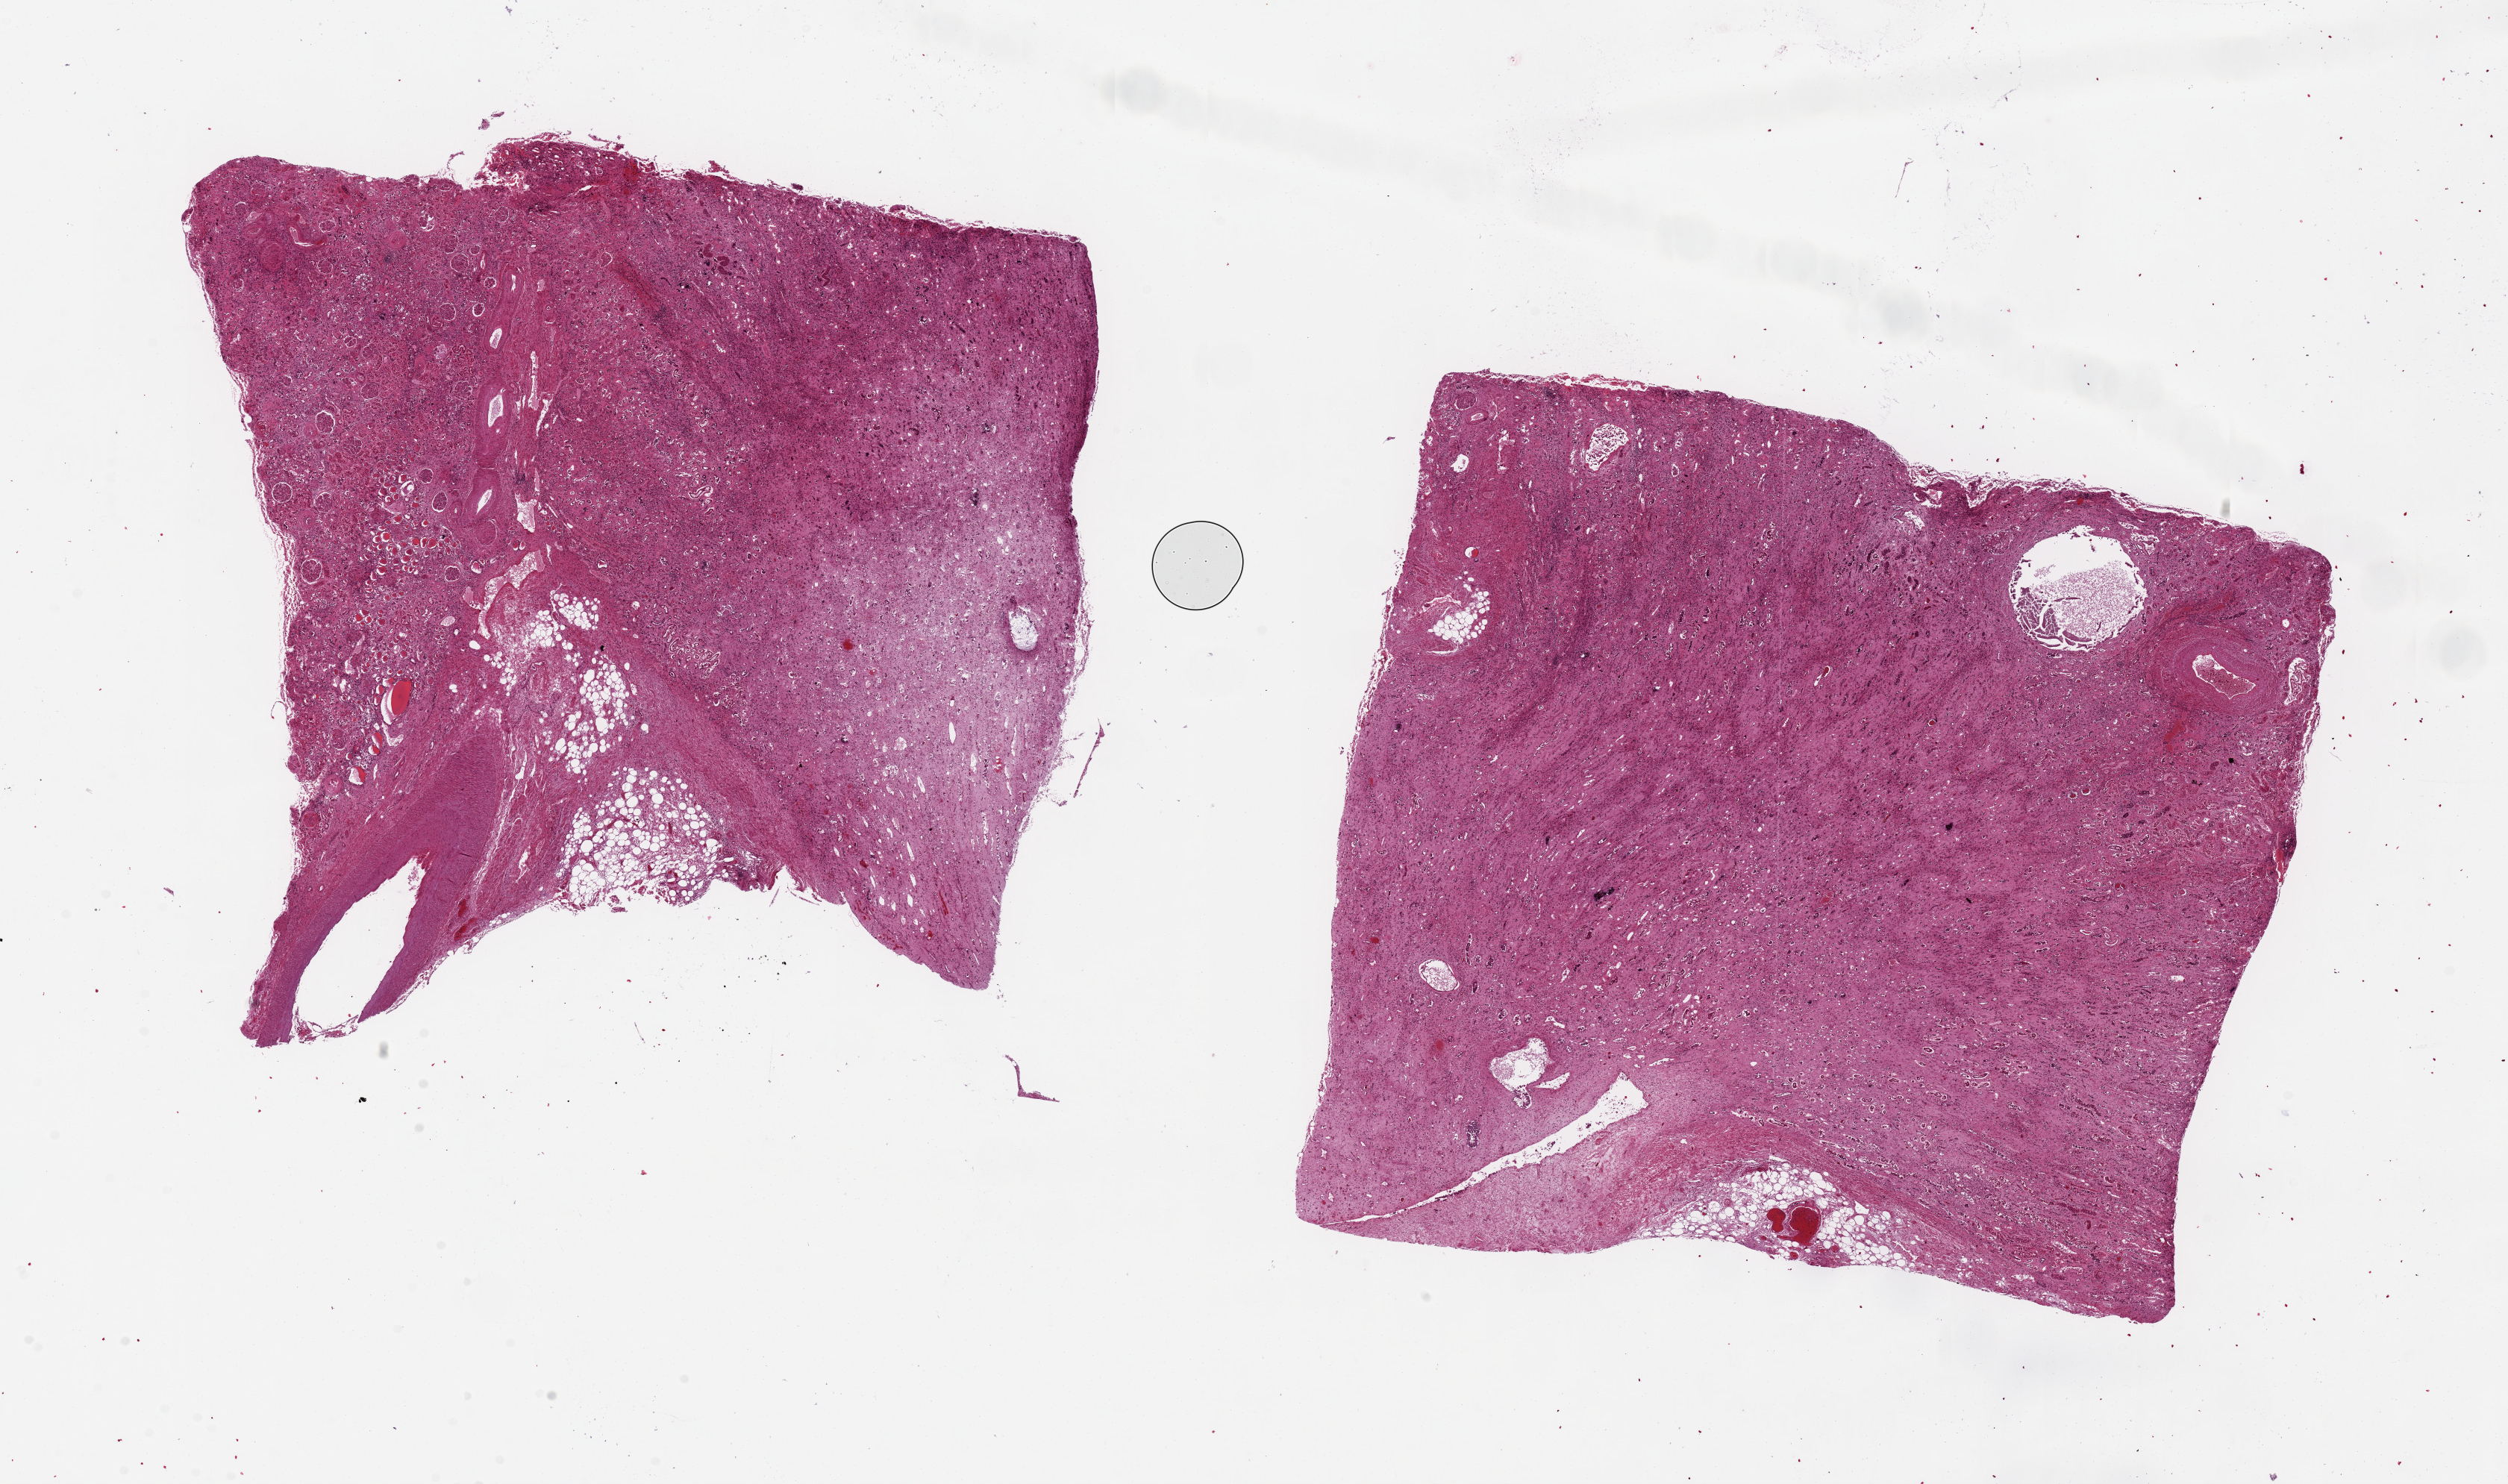
Whole-slide image, hematoxylin and eosin (H&E) stain — whole scanned area (about 26.6 x 15.7 mm) shown as a low-resolution overview. PAXgene-fixed paraffin-embedded (PFPE) section. Sampled site (target tissue): renal medulla. Tissue donor sample.
• reviewer comment on this tissue sample: 2 ~10x8mm aliquots. Contaminant glomeruli in one aliquot, ~40%. Chronic/fibrosing intersitital nephritis; focal areas of ???thyroidization???